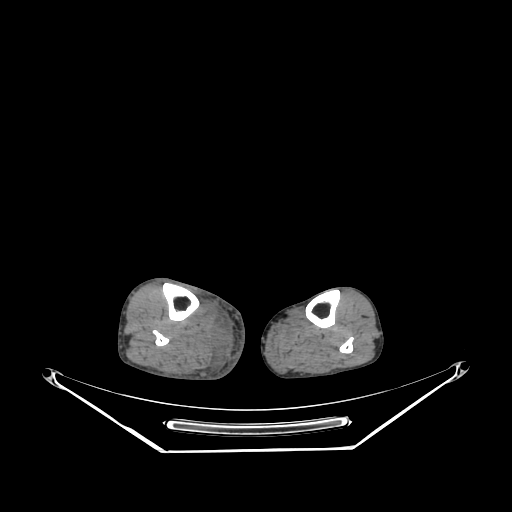
CT of an extremity soft-tissue mass (from a PET/CT study), one axial slice; position 123 of 267 along the scan axis; reconstruction kernel SOFT; 140 kVp; soft-tissue window (W 400 / L 40 HU); 3.75 mm slice thickness; 512 × 512 image matrix. Male patient. Case-level facts recorded for this patient, not image findings: histological type: pleiomorphic liposarcoma; grade: high; site of the primary tumour: right calf.
Annotated regions visible in this slice (expert contour drawn on MRI and transferred to this co-registered scan by the dataset authors):
- gross tumour volume including surrounding oedema: box from (x=208, y=319) to (x=232, y=357) px